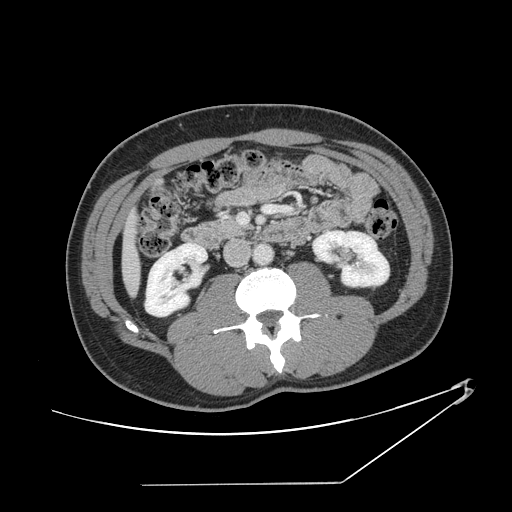
Contrast-enhanced abdominal CT, one axial slice. Slice 45 of 152 in the series (ordered by position). Intravenous contrast given. Soft-tissue window (W 400 / L 40 HU). 2.5 mm slice thickness. 512 × 512 image matrix. Male patient, age 45 years. From the clinical record (not read from this slice): diagnosis: colorectal cancer liver metastases, imaged before liver resection; multiple liver metastases: no; largest metastasis: 1 cm; disease in both lobes: no.
Annotated regions visible in this slice (outlined manually by an expert reader):
- liver: bounding box (x1, y1, x2, y2) in pixels: (124, 222, 140, 292)
- planned liver remnant (the part of the liver to remain after resection): (124, 221, 140, 292)
- portal vein (with intrahepatic branches): (239, 205, 290, 224)